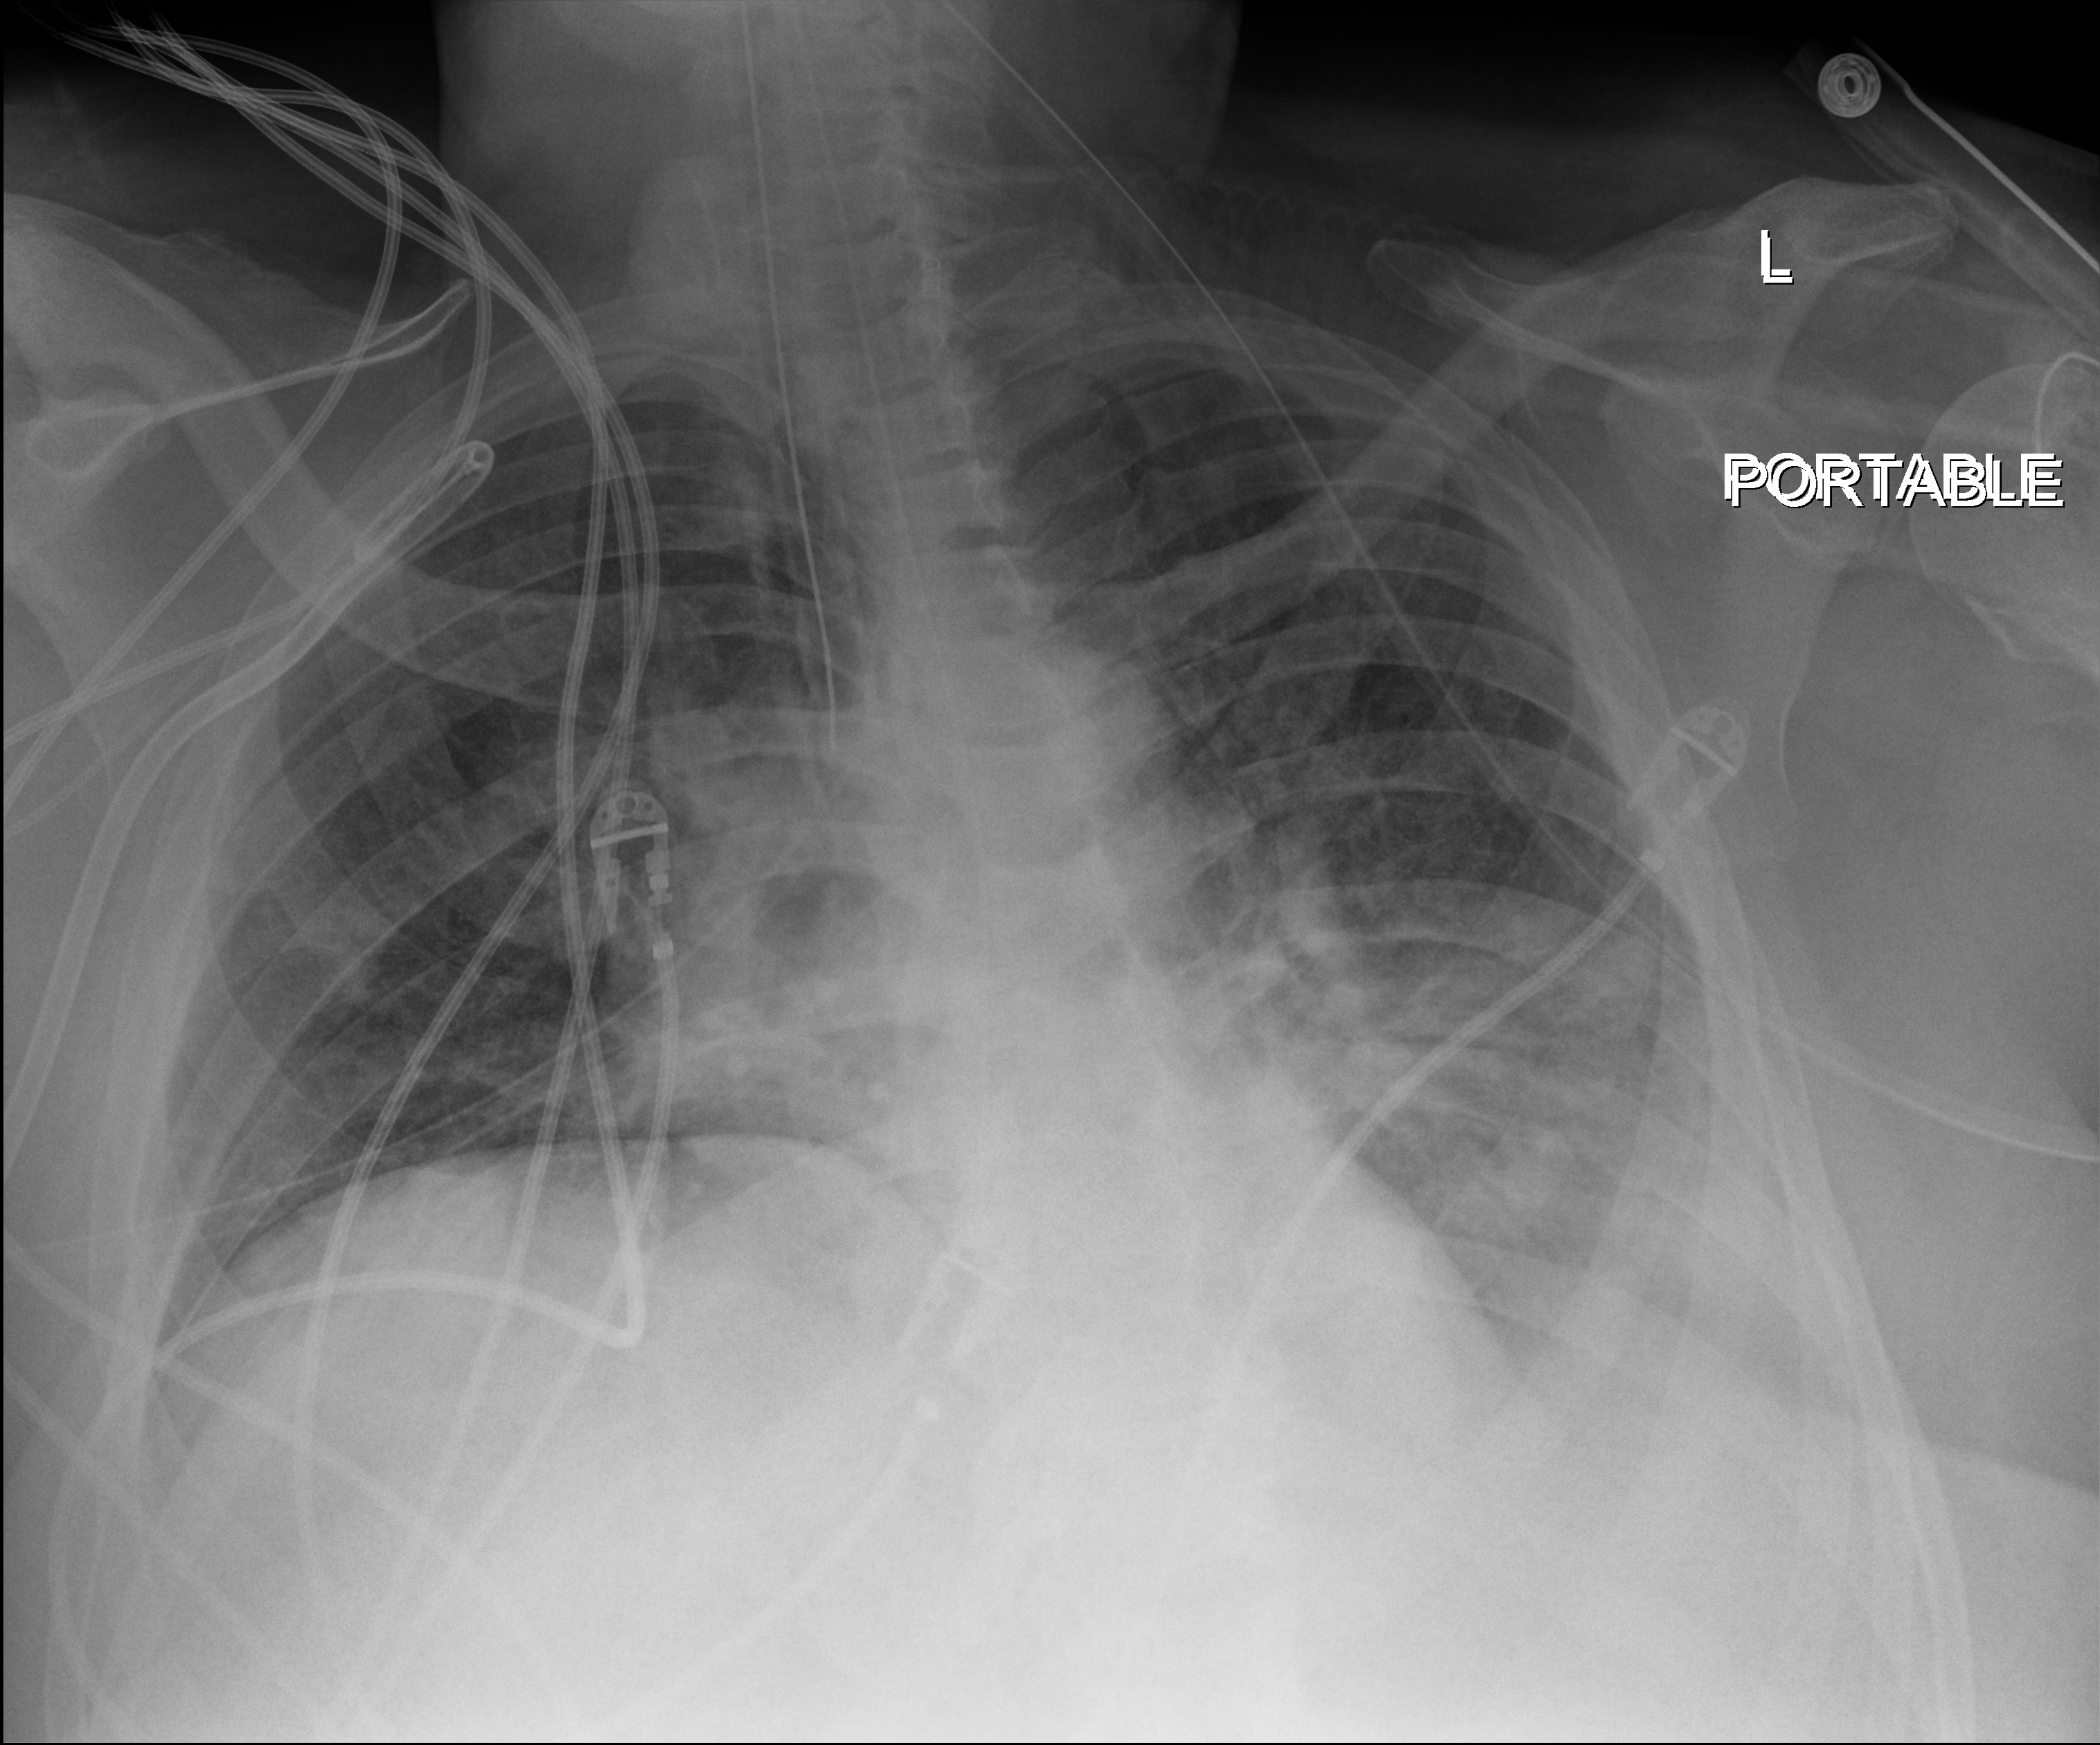
Bedside chest radiograph (digital radiography); anteroposterior (AP) projection. Patient hospitalised with COVID-19; male, aged 60–74 years.
Hospital-stay facts (about this admission, not read from this image; timing relative to this image not recorded):
- admitted to intensive care during this hospital stay: yes